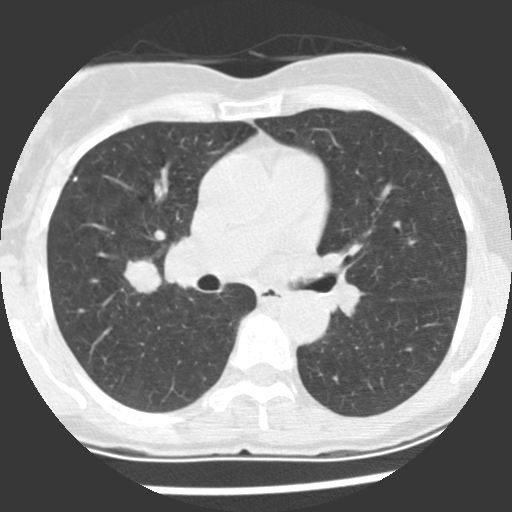
Low-dose screening chest CT, one axial slice; position 125 of 225 along the scan axis; reconstruction kernel STANDARD; 120 kVp; lung window (W 1500 / L -600 HU); 2.5 mm slice thickness; 512 × 512 image matrix, field of view 270 × 270 mm.
Outlined on this slice (outlined manually by an expert reader):
- lesion 1 (tumor, upper lobe of right lung): bounding box (x1, y1, x2, y2) in pixels: (124, 259, 161, 294)